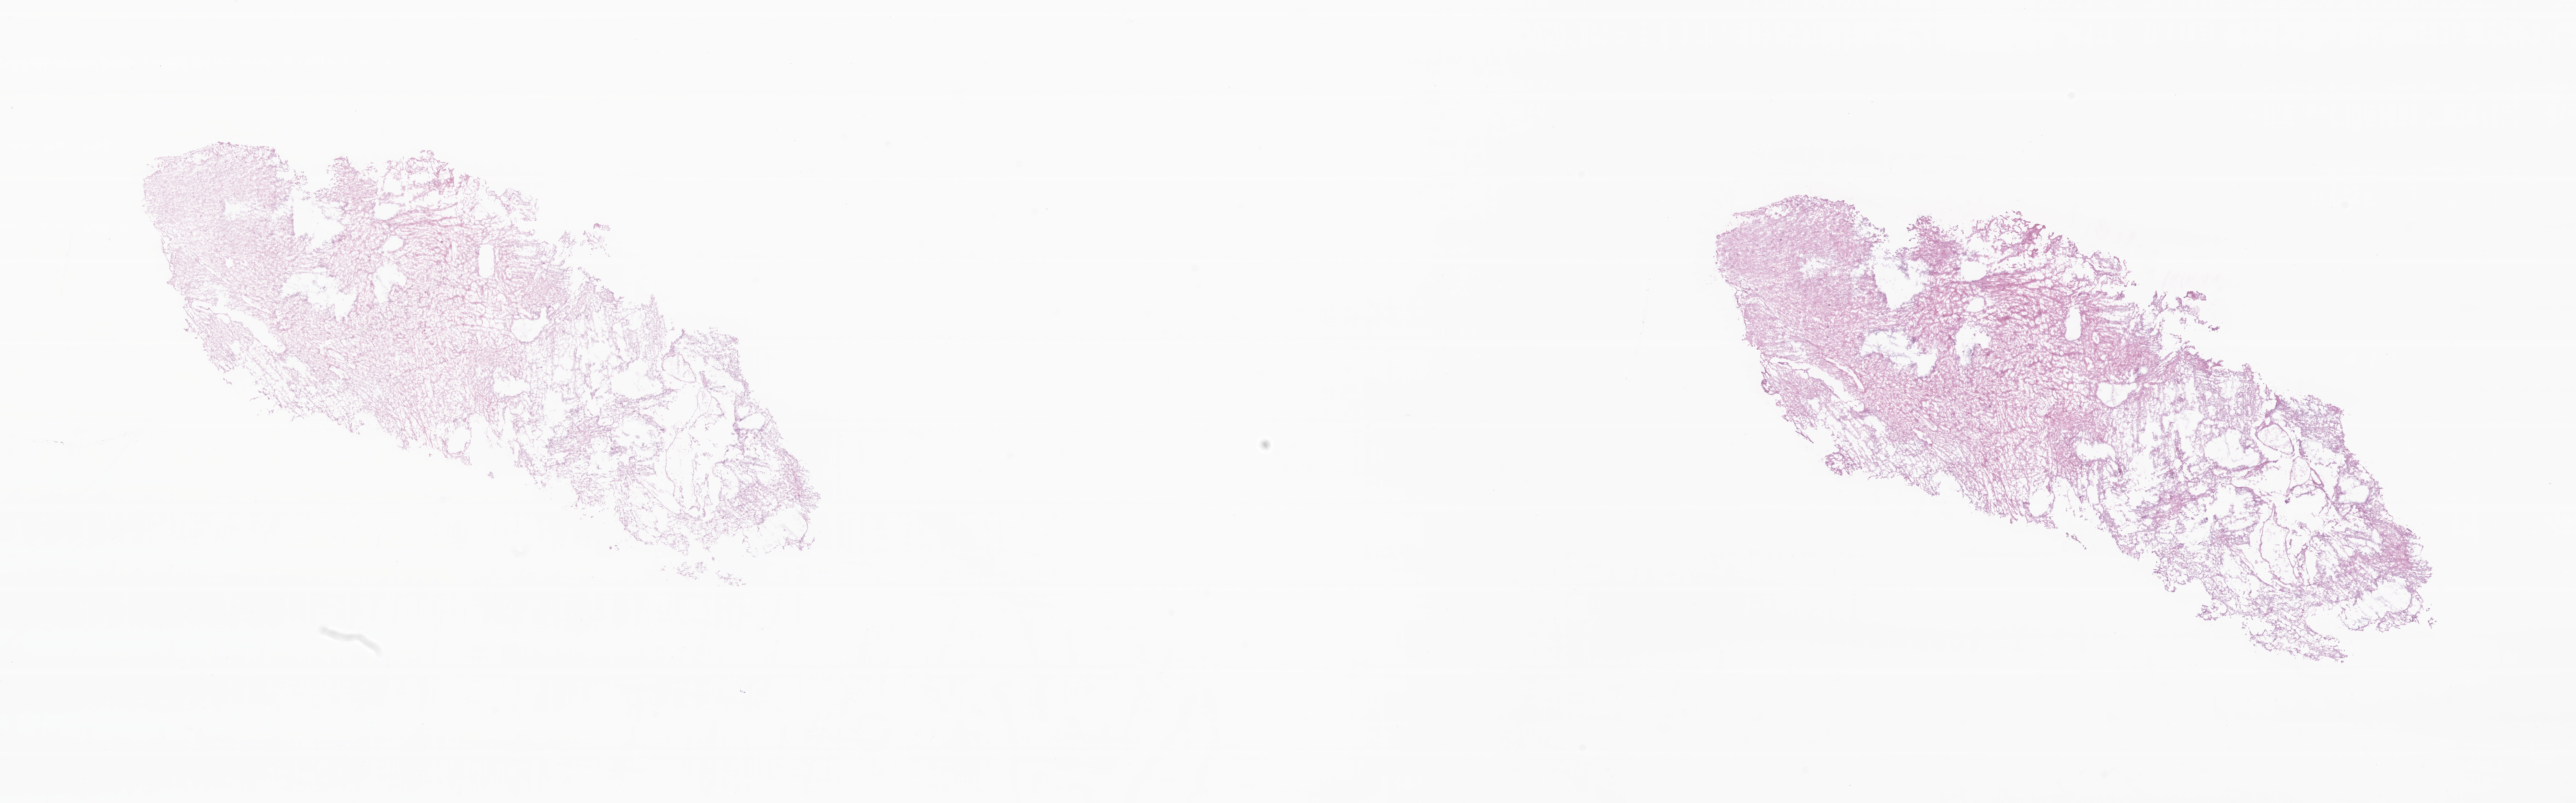
H&E whole-slide image of tumor tissue from the cerebellum — whole scanned area (about 33.5 x 10.4 mm) shown as a low-resolution overview. Cryosection (OCT / tissue freezing medium). Patient: female, age 59 months (4 years 11 months).
Diagnosis: Pilocytic astrocytoma.